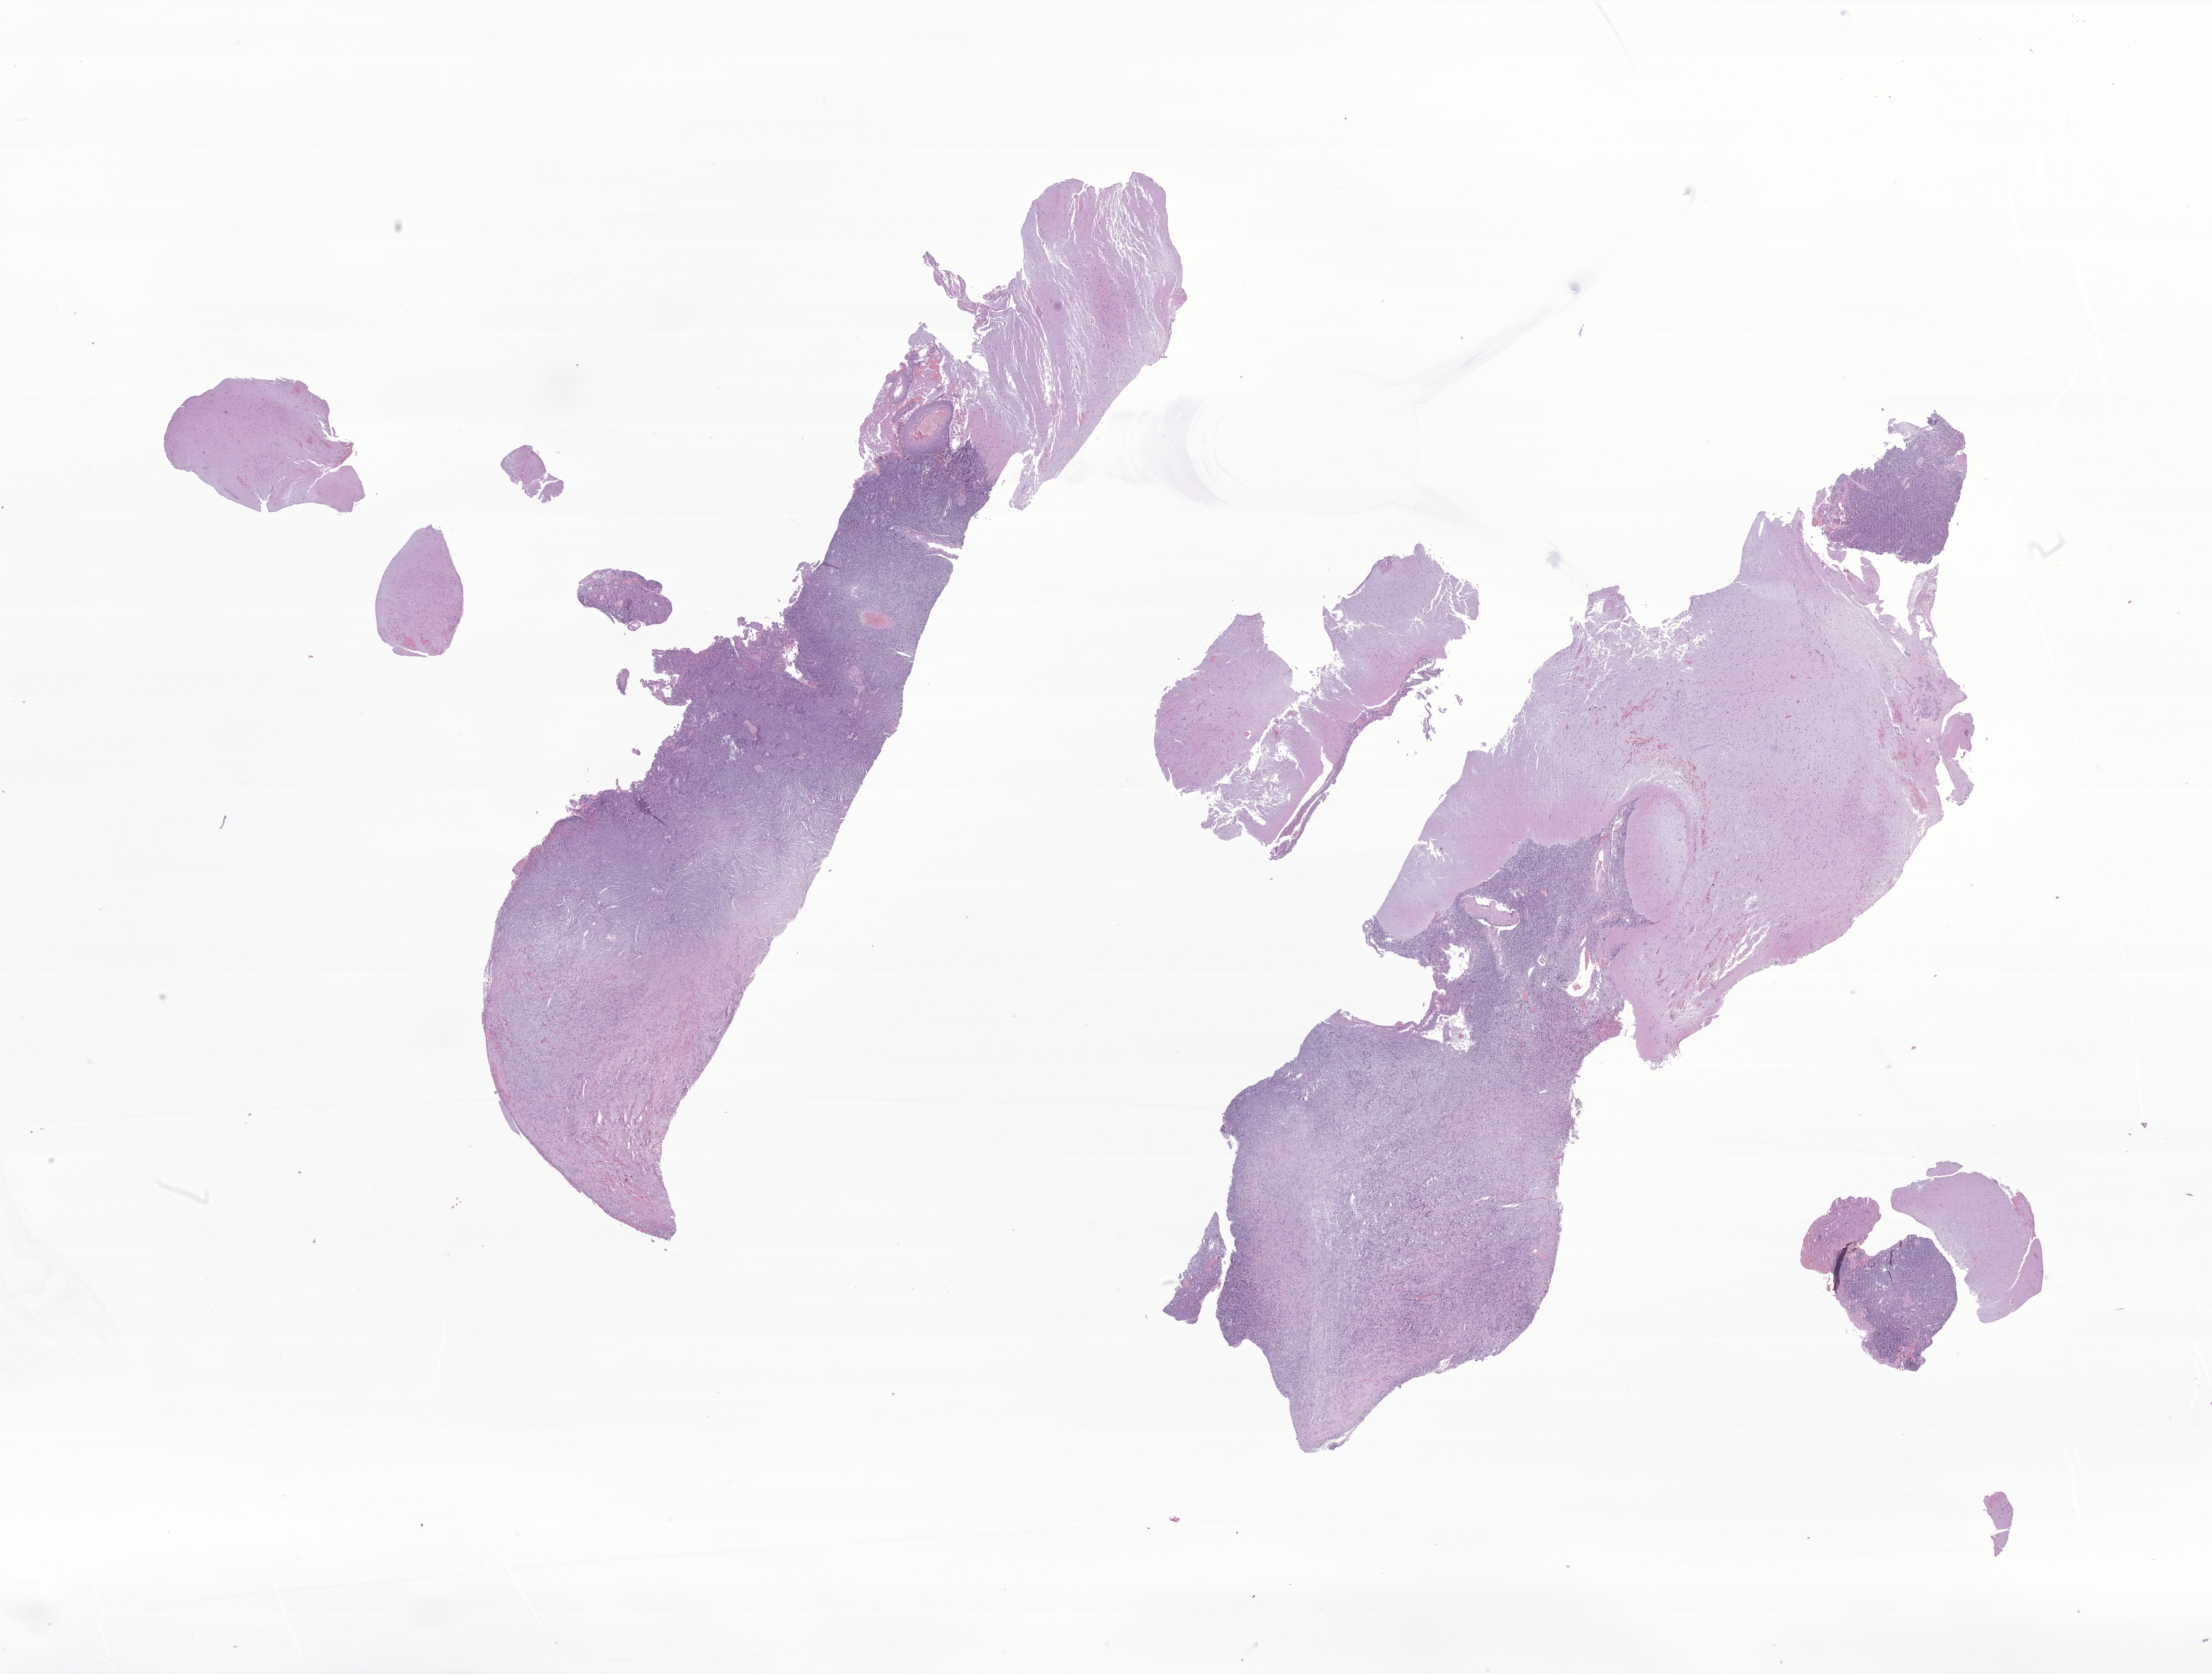
H&E whole-slide image of tumor tissue from the occipital lobe, whole scanned area (about 25.8 x 19.5 mm) shown as a low-resolution overview, FFPE section. Patient: male, age 202 days.
Recorded diagnosis: Spindle cell carcinoma, NOS.